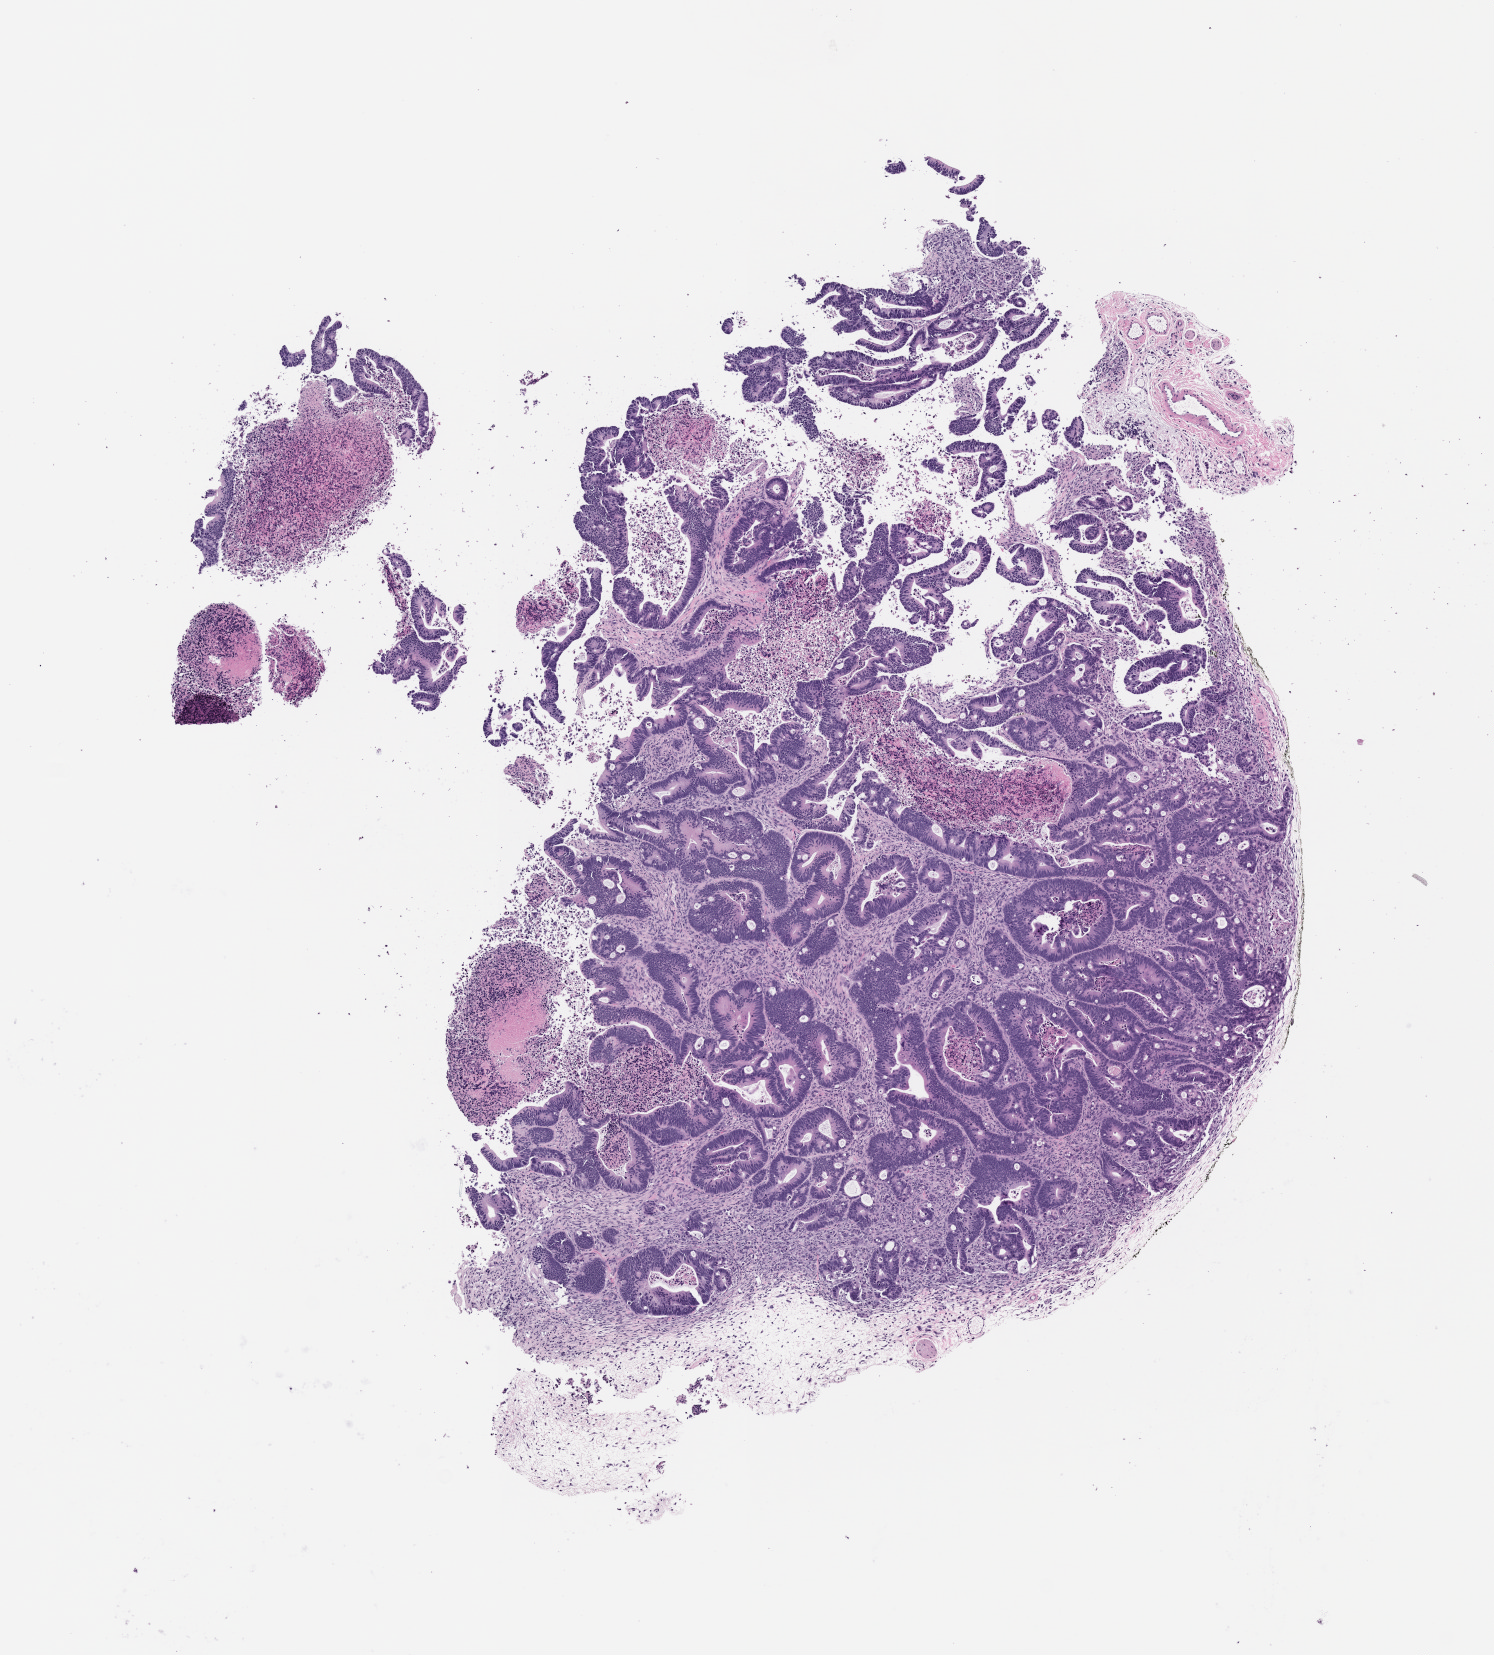
Whole-slide image, haematoxylin and eosin: patient-derived xenograft (human tumor grown in a mouse), passage 4, whole scanned area (about 6.0 x 6.7 mm) shown as a low-resolution overview. Formalin-fixed, paraffin-embedded (FFPE) tissue. Tumor site category: colon.
- originating patient diagnosis: Colon Adenocarcinoma